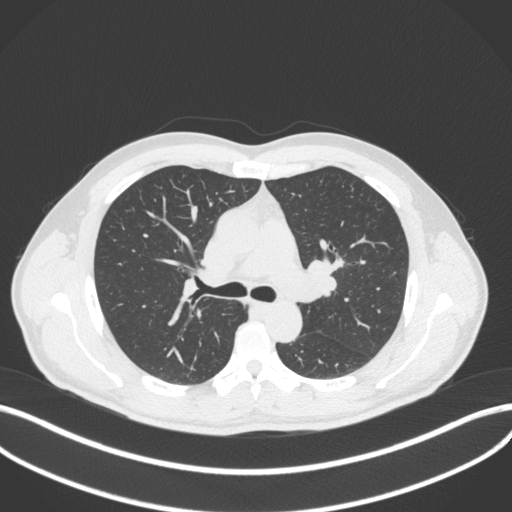
Chest CT, one axial slice; position 271 of 383 along the scan axis; reconstruction kernel B31f; 120 kVp; lung window (W 1500 / L -600 HU); 1 mm slice thickness; 512 × 512 image matrix, field of view 400 × 400 mm. Male patient, age 50 years. From the clinical record (not read from this slice): clinical TNM (as recorded): T1c N1 M1b.
Outlined on this slice (bounding box drawn by a radiologist):
- lung tumour (recorded histology: squamous cell carcinoma): bounding box <328,247,345,273> (left, top, right, bottom; pixels)